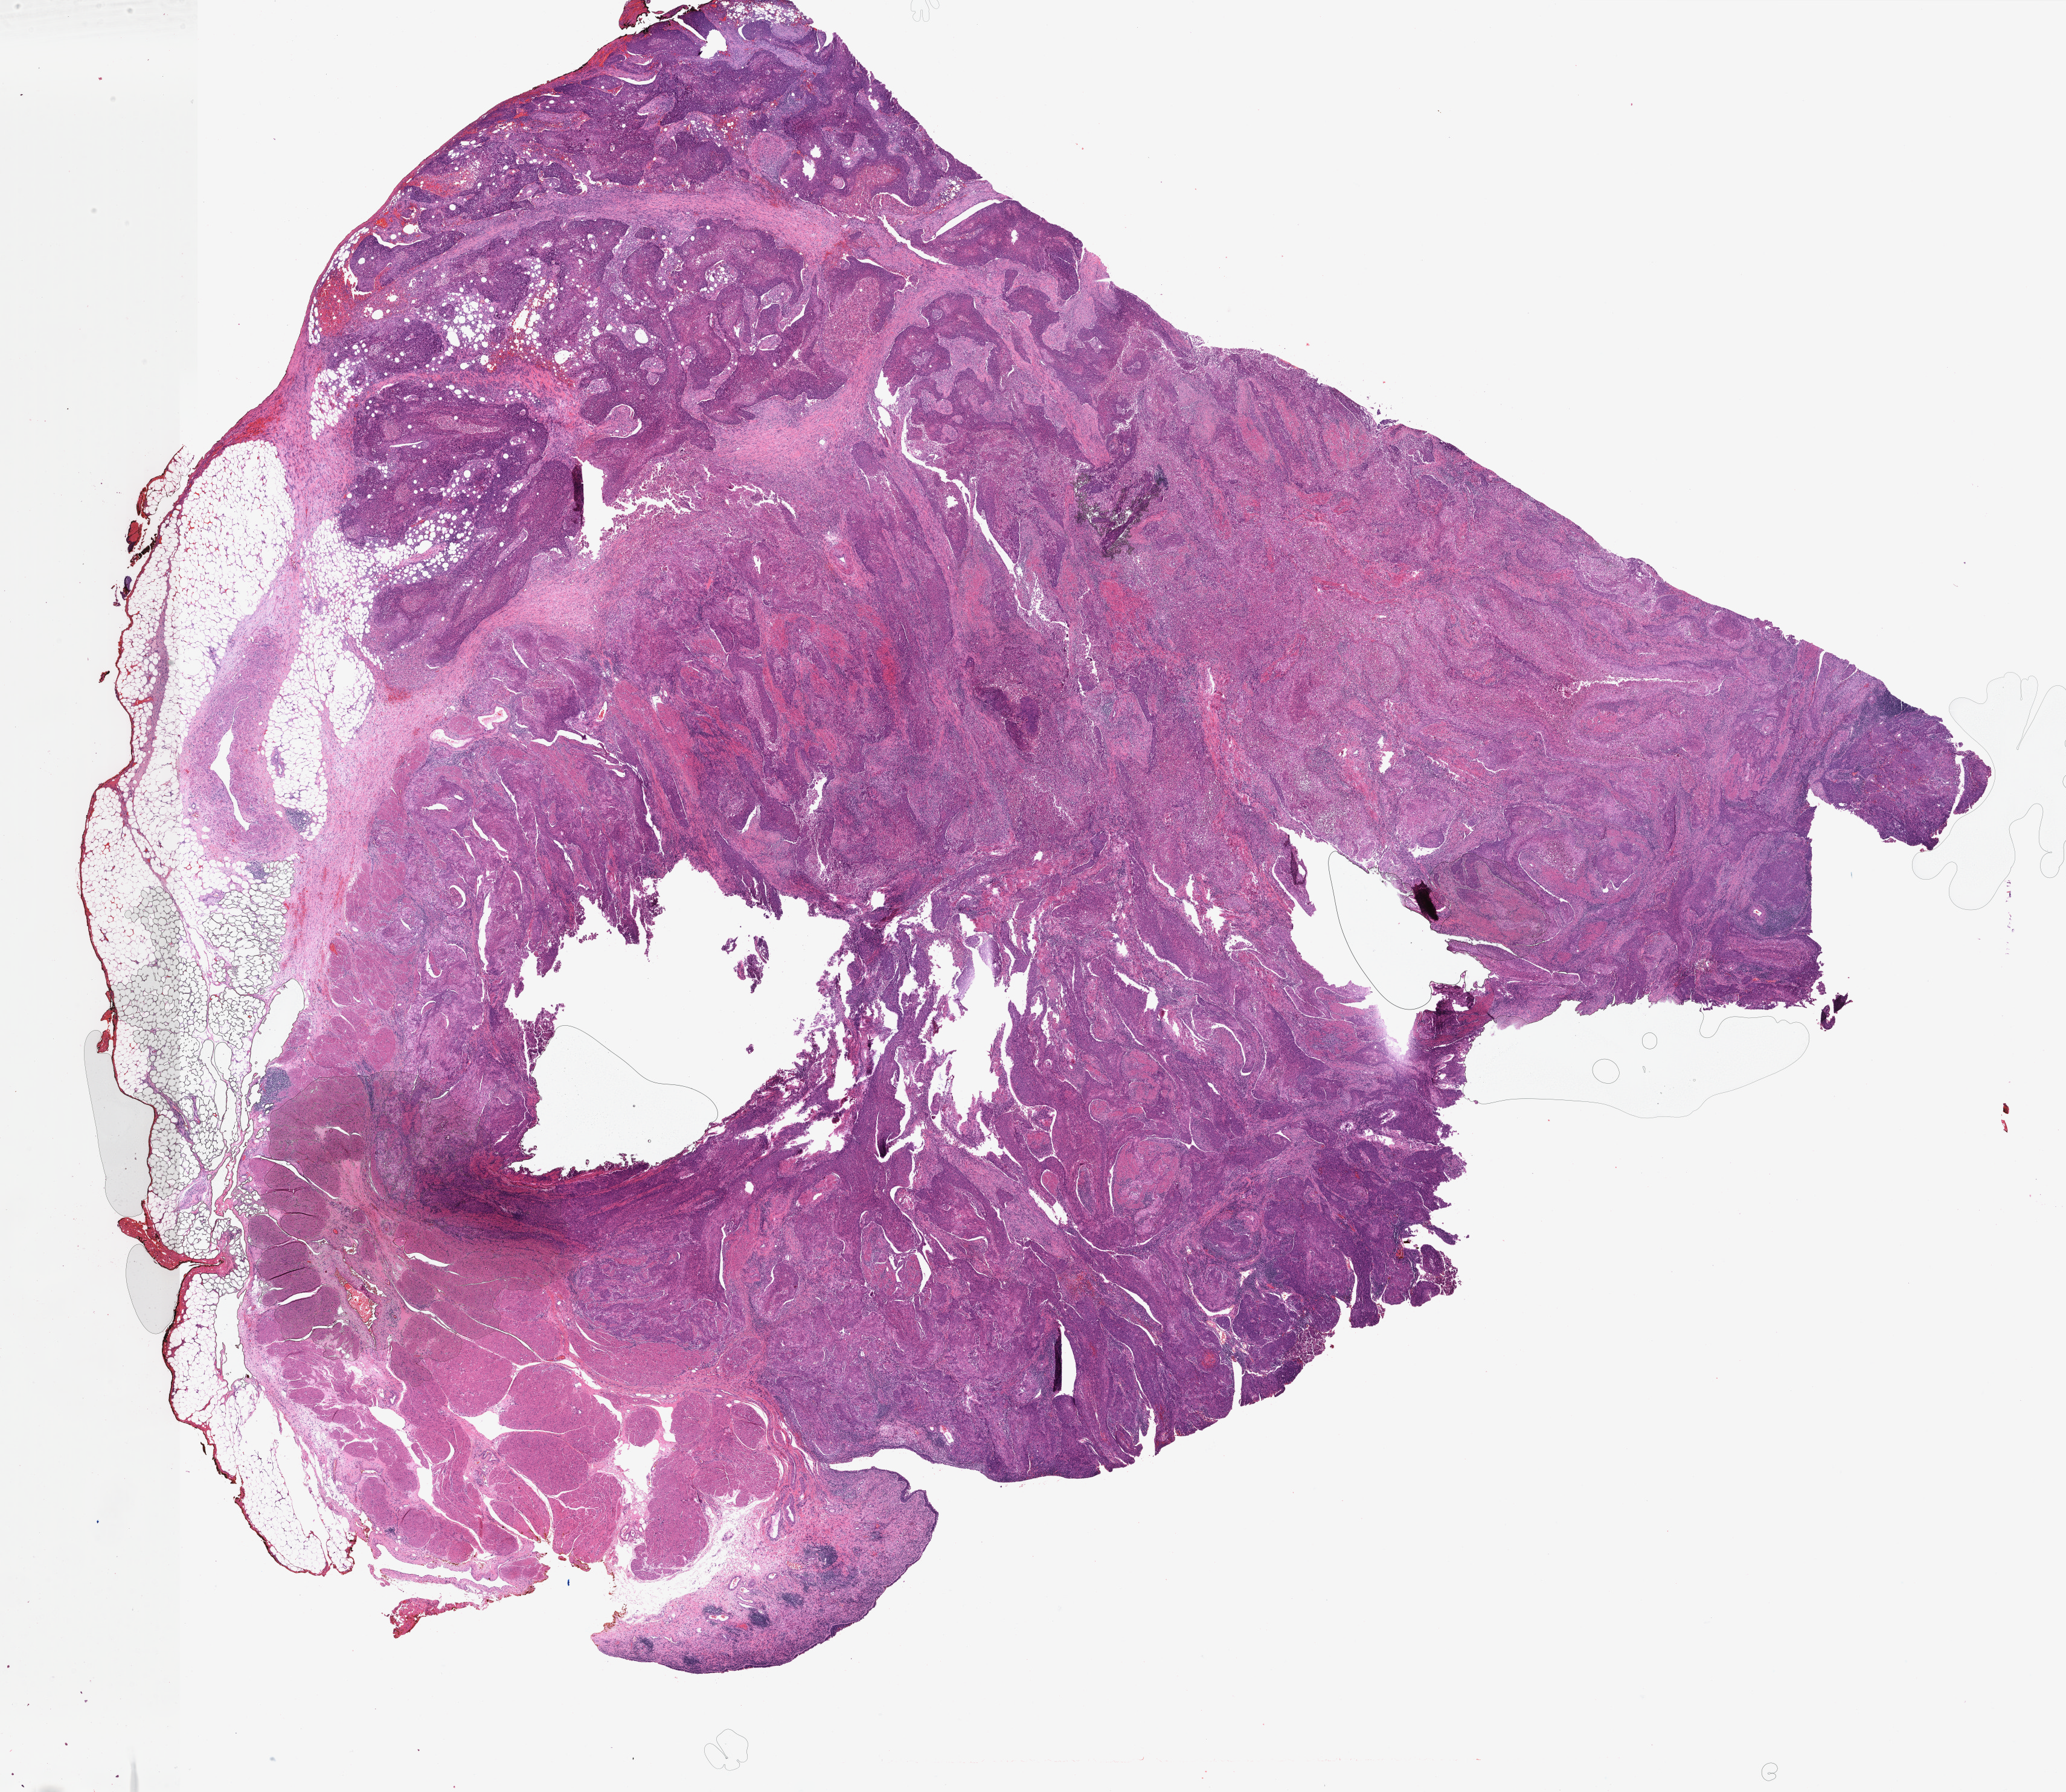
Digitized H&E tissue section (whole slide) — low-resolution overview of the scanned area, about 27.2 x 23.6 mm (from a 40x scan), FFPE section, bladder, primary tumour sample. Female, age 70 years at initial diagnosis. Histologic grade: high grade.
• AJCC pathologic stage: III (6th edition)
• lymph nodes positive (case pathology): 0 of 14 examined
• histologic diagnosis: Transitional cell carcinoma